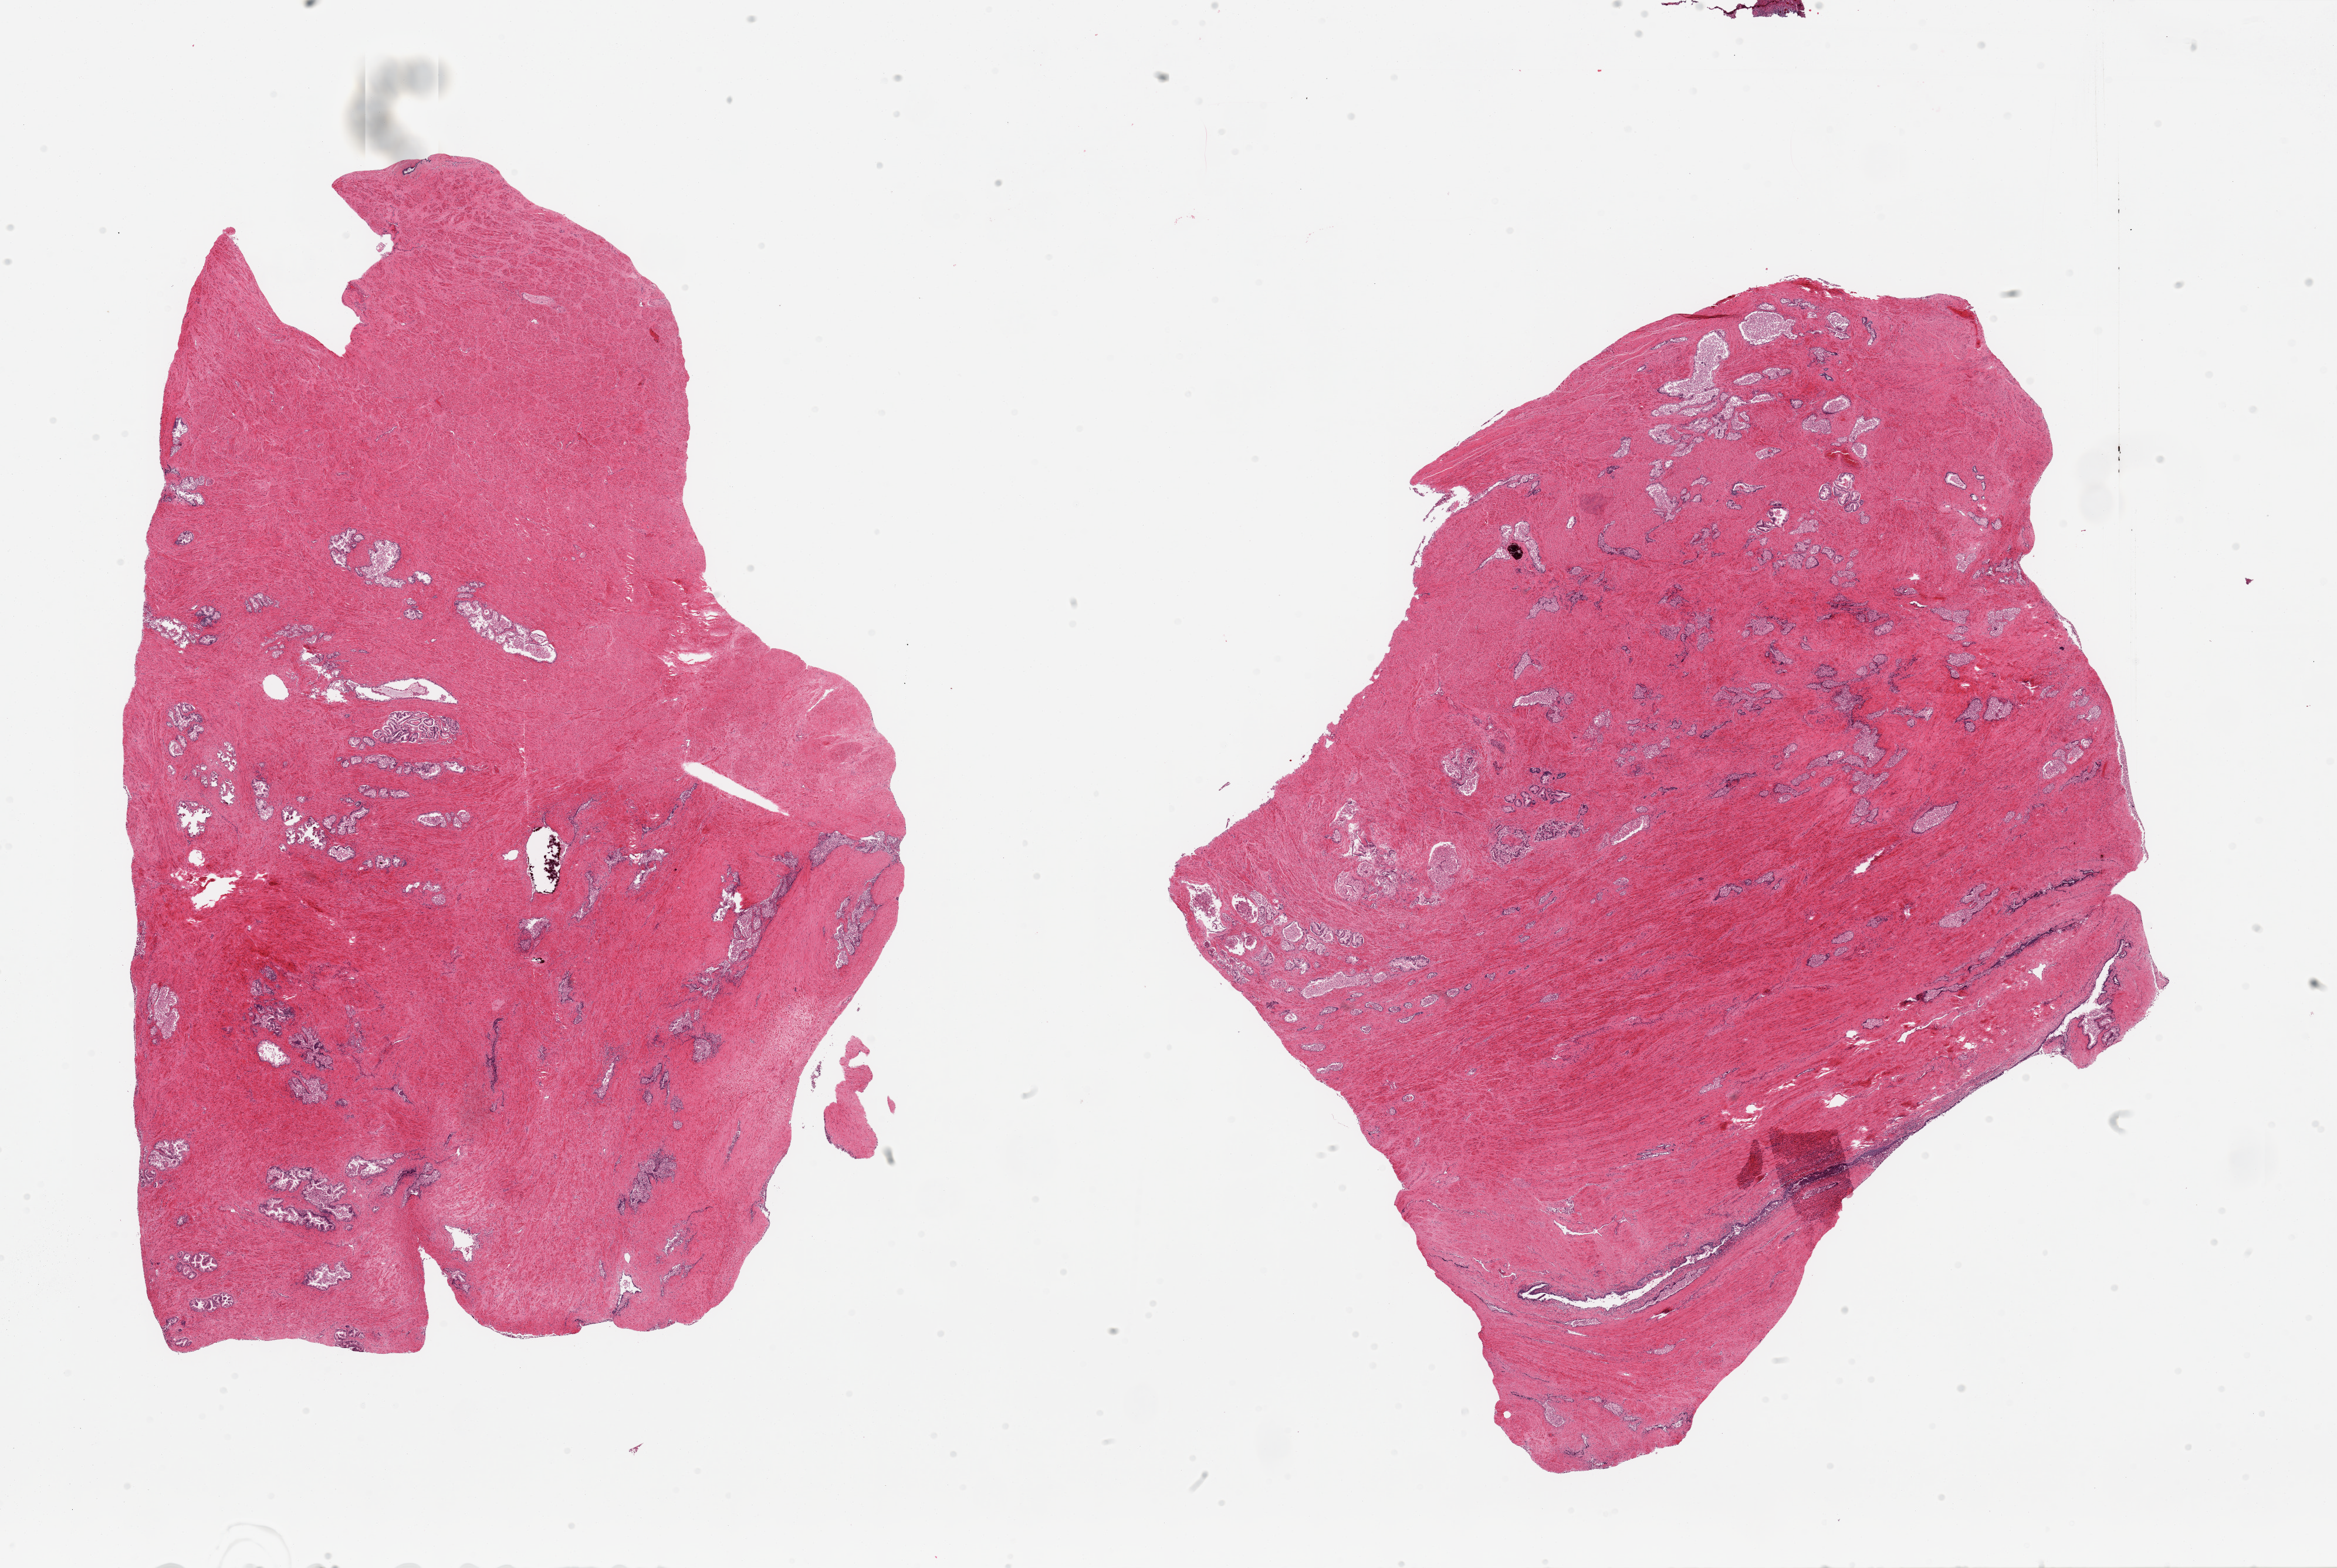
Haematoxylin and eosin whole-slide image — a low-resolution overview of the entire scanned area, about 31.5 x 21.1 mm (slide scanned at 20x), PAXgene-fixed, paraffin-embedded tissue, section of prostate (target tissue), donor tissue sample. Male donor.
Review note (as recorded): 2 pieces, glandular epithelium with advance autolysis.